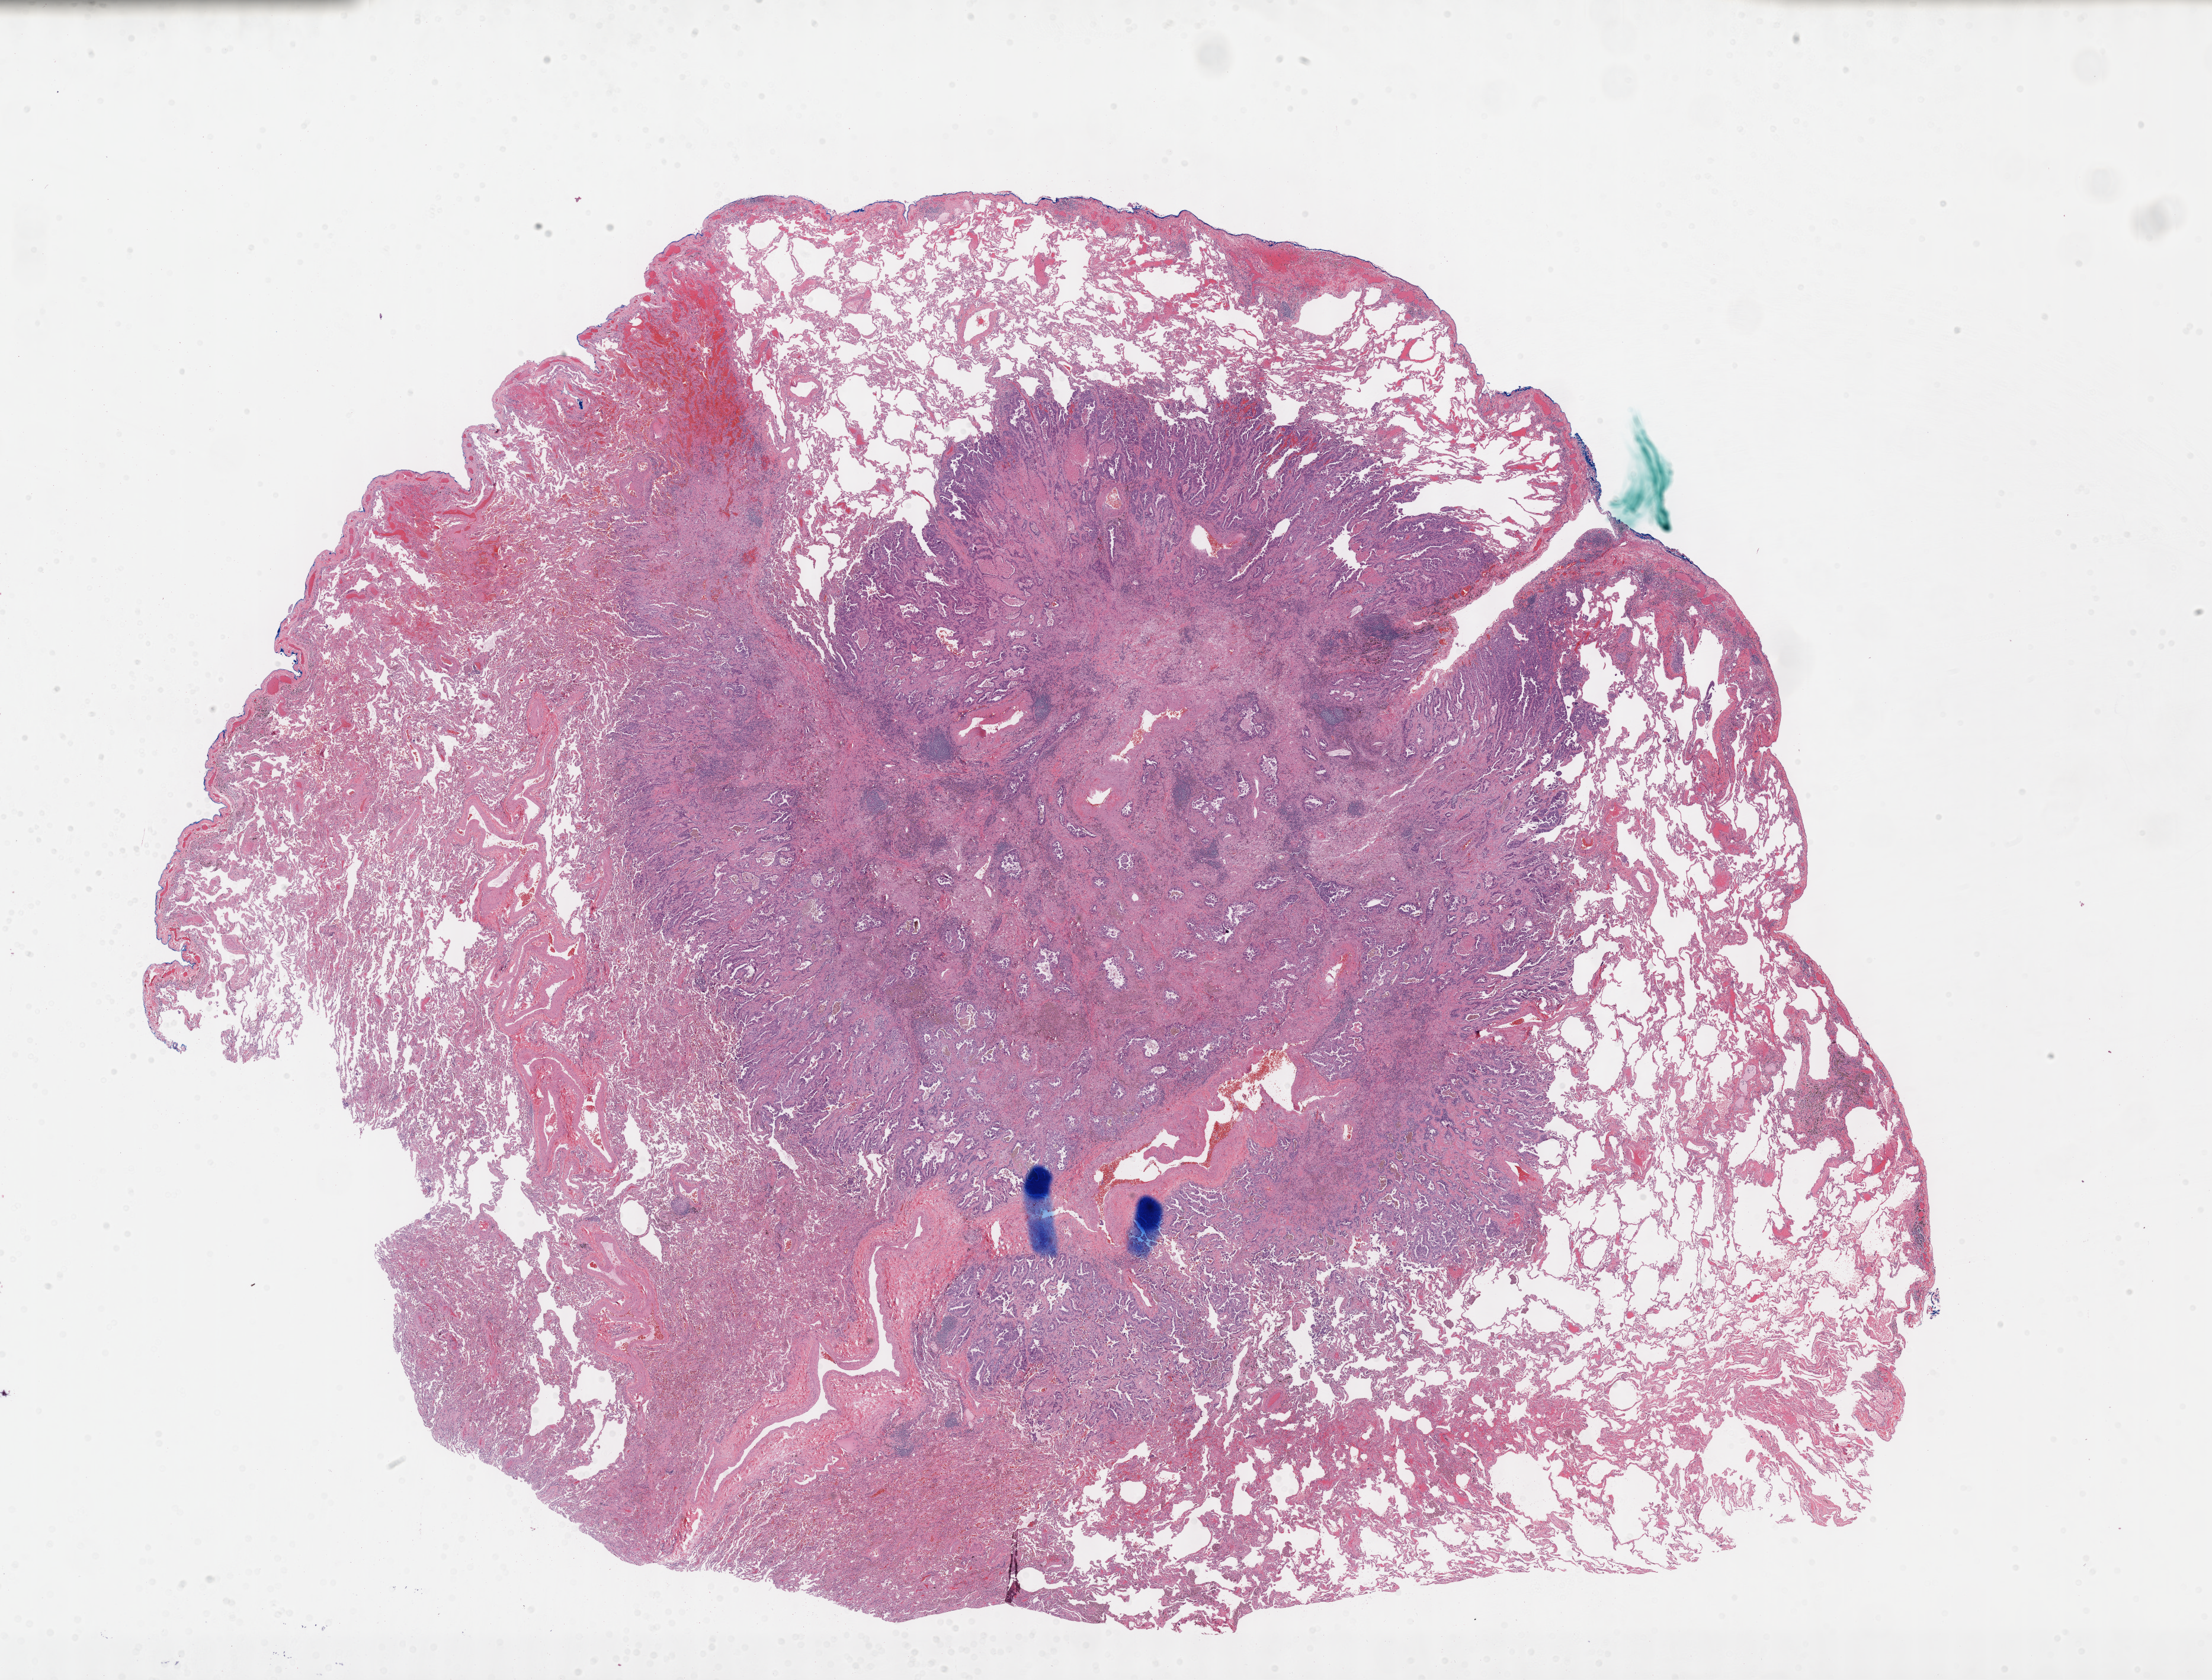
Whole-slide histology image, H&E-stained, a low-resolution overview of the entire scanned area, about 30.2 x 22.9 mm (slide scanned at 40x); FFPE section; sample: primary tumour, lung. Male patient; age at initial diagnosis 57 years.
AJCC pathologic stage: IA. Pathologic diagnosis: Adenocarcinoma, NOS.